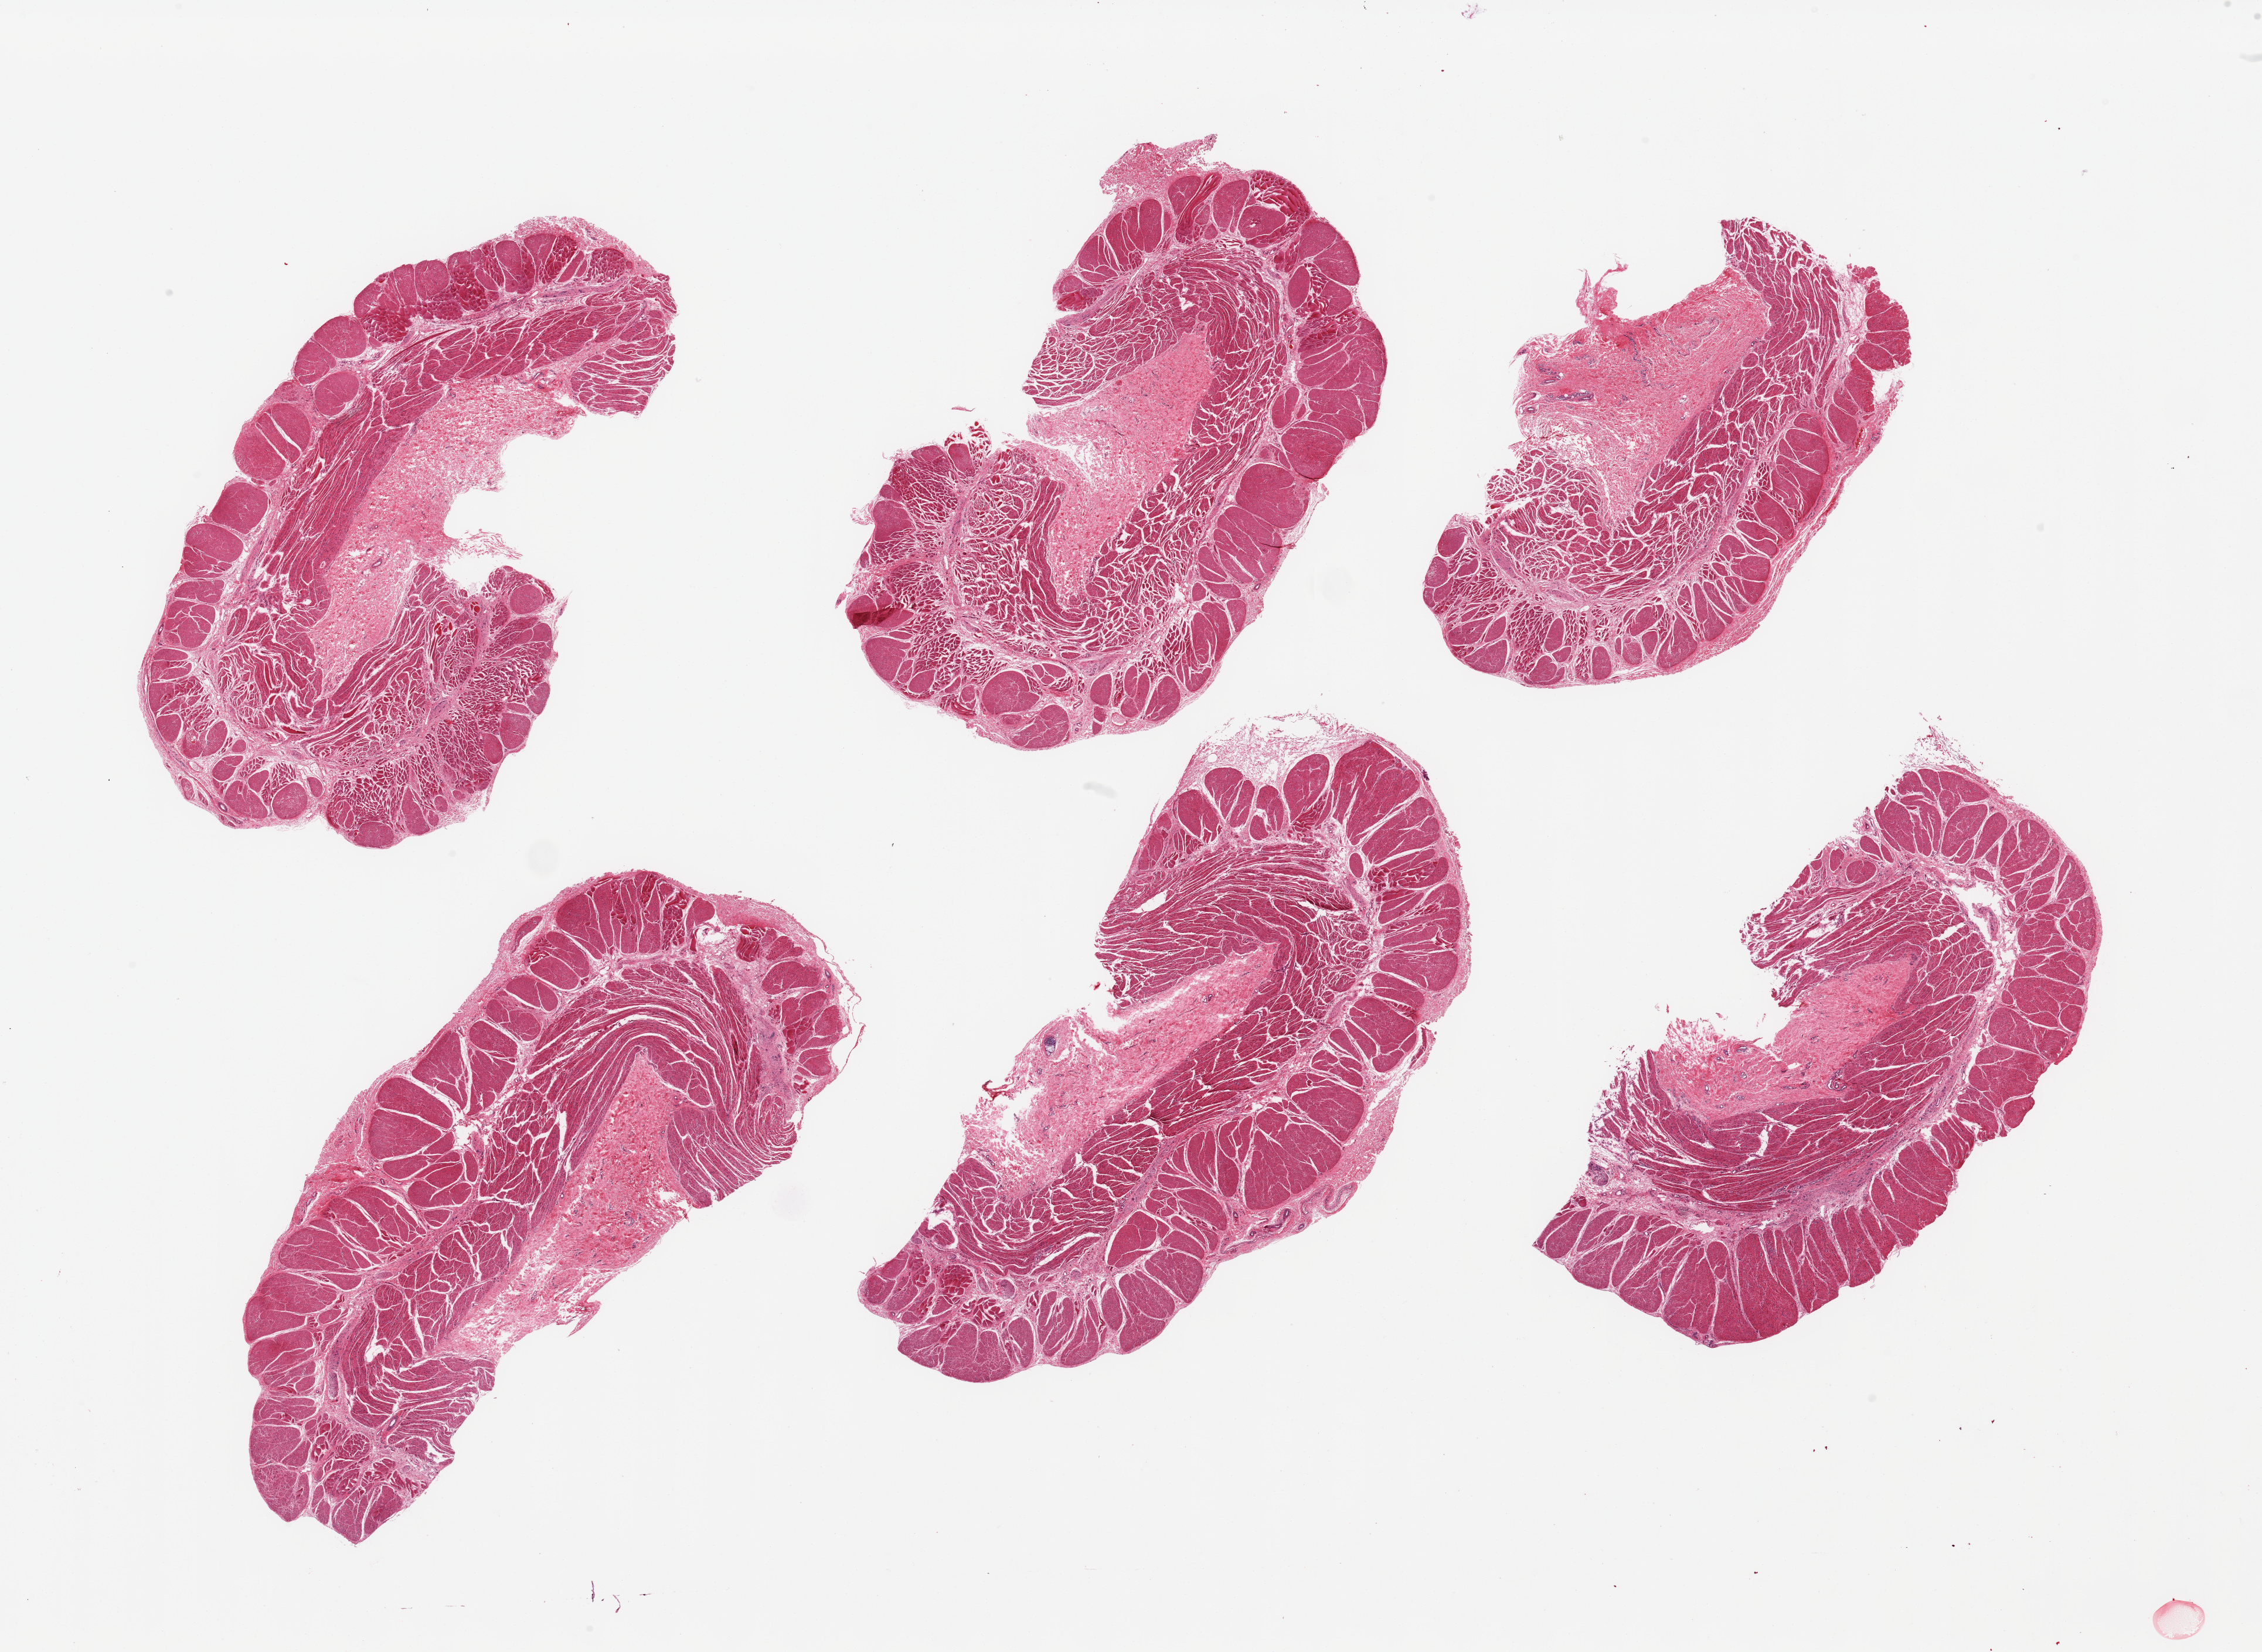
Digitized haematoxylin and eosin-stained section, brightfield — low-resolution overview of the scanned area, about 30.5 x 22.3 mm (acquisition: 20x scan), PAXgene-fixed paraffin-embedded (PFPE) section, sampled site (target tissue): esophageal muscle, tissue donor sample.
- review note (as recorded): 6 pieces; muscularis with significant admixture of smooth and skeletal muscle suggesting sampling of upper esophagus